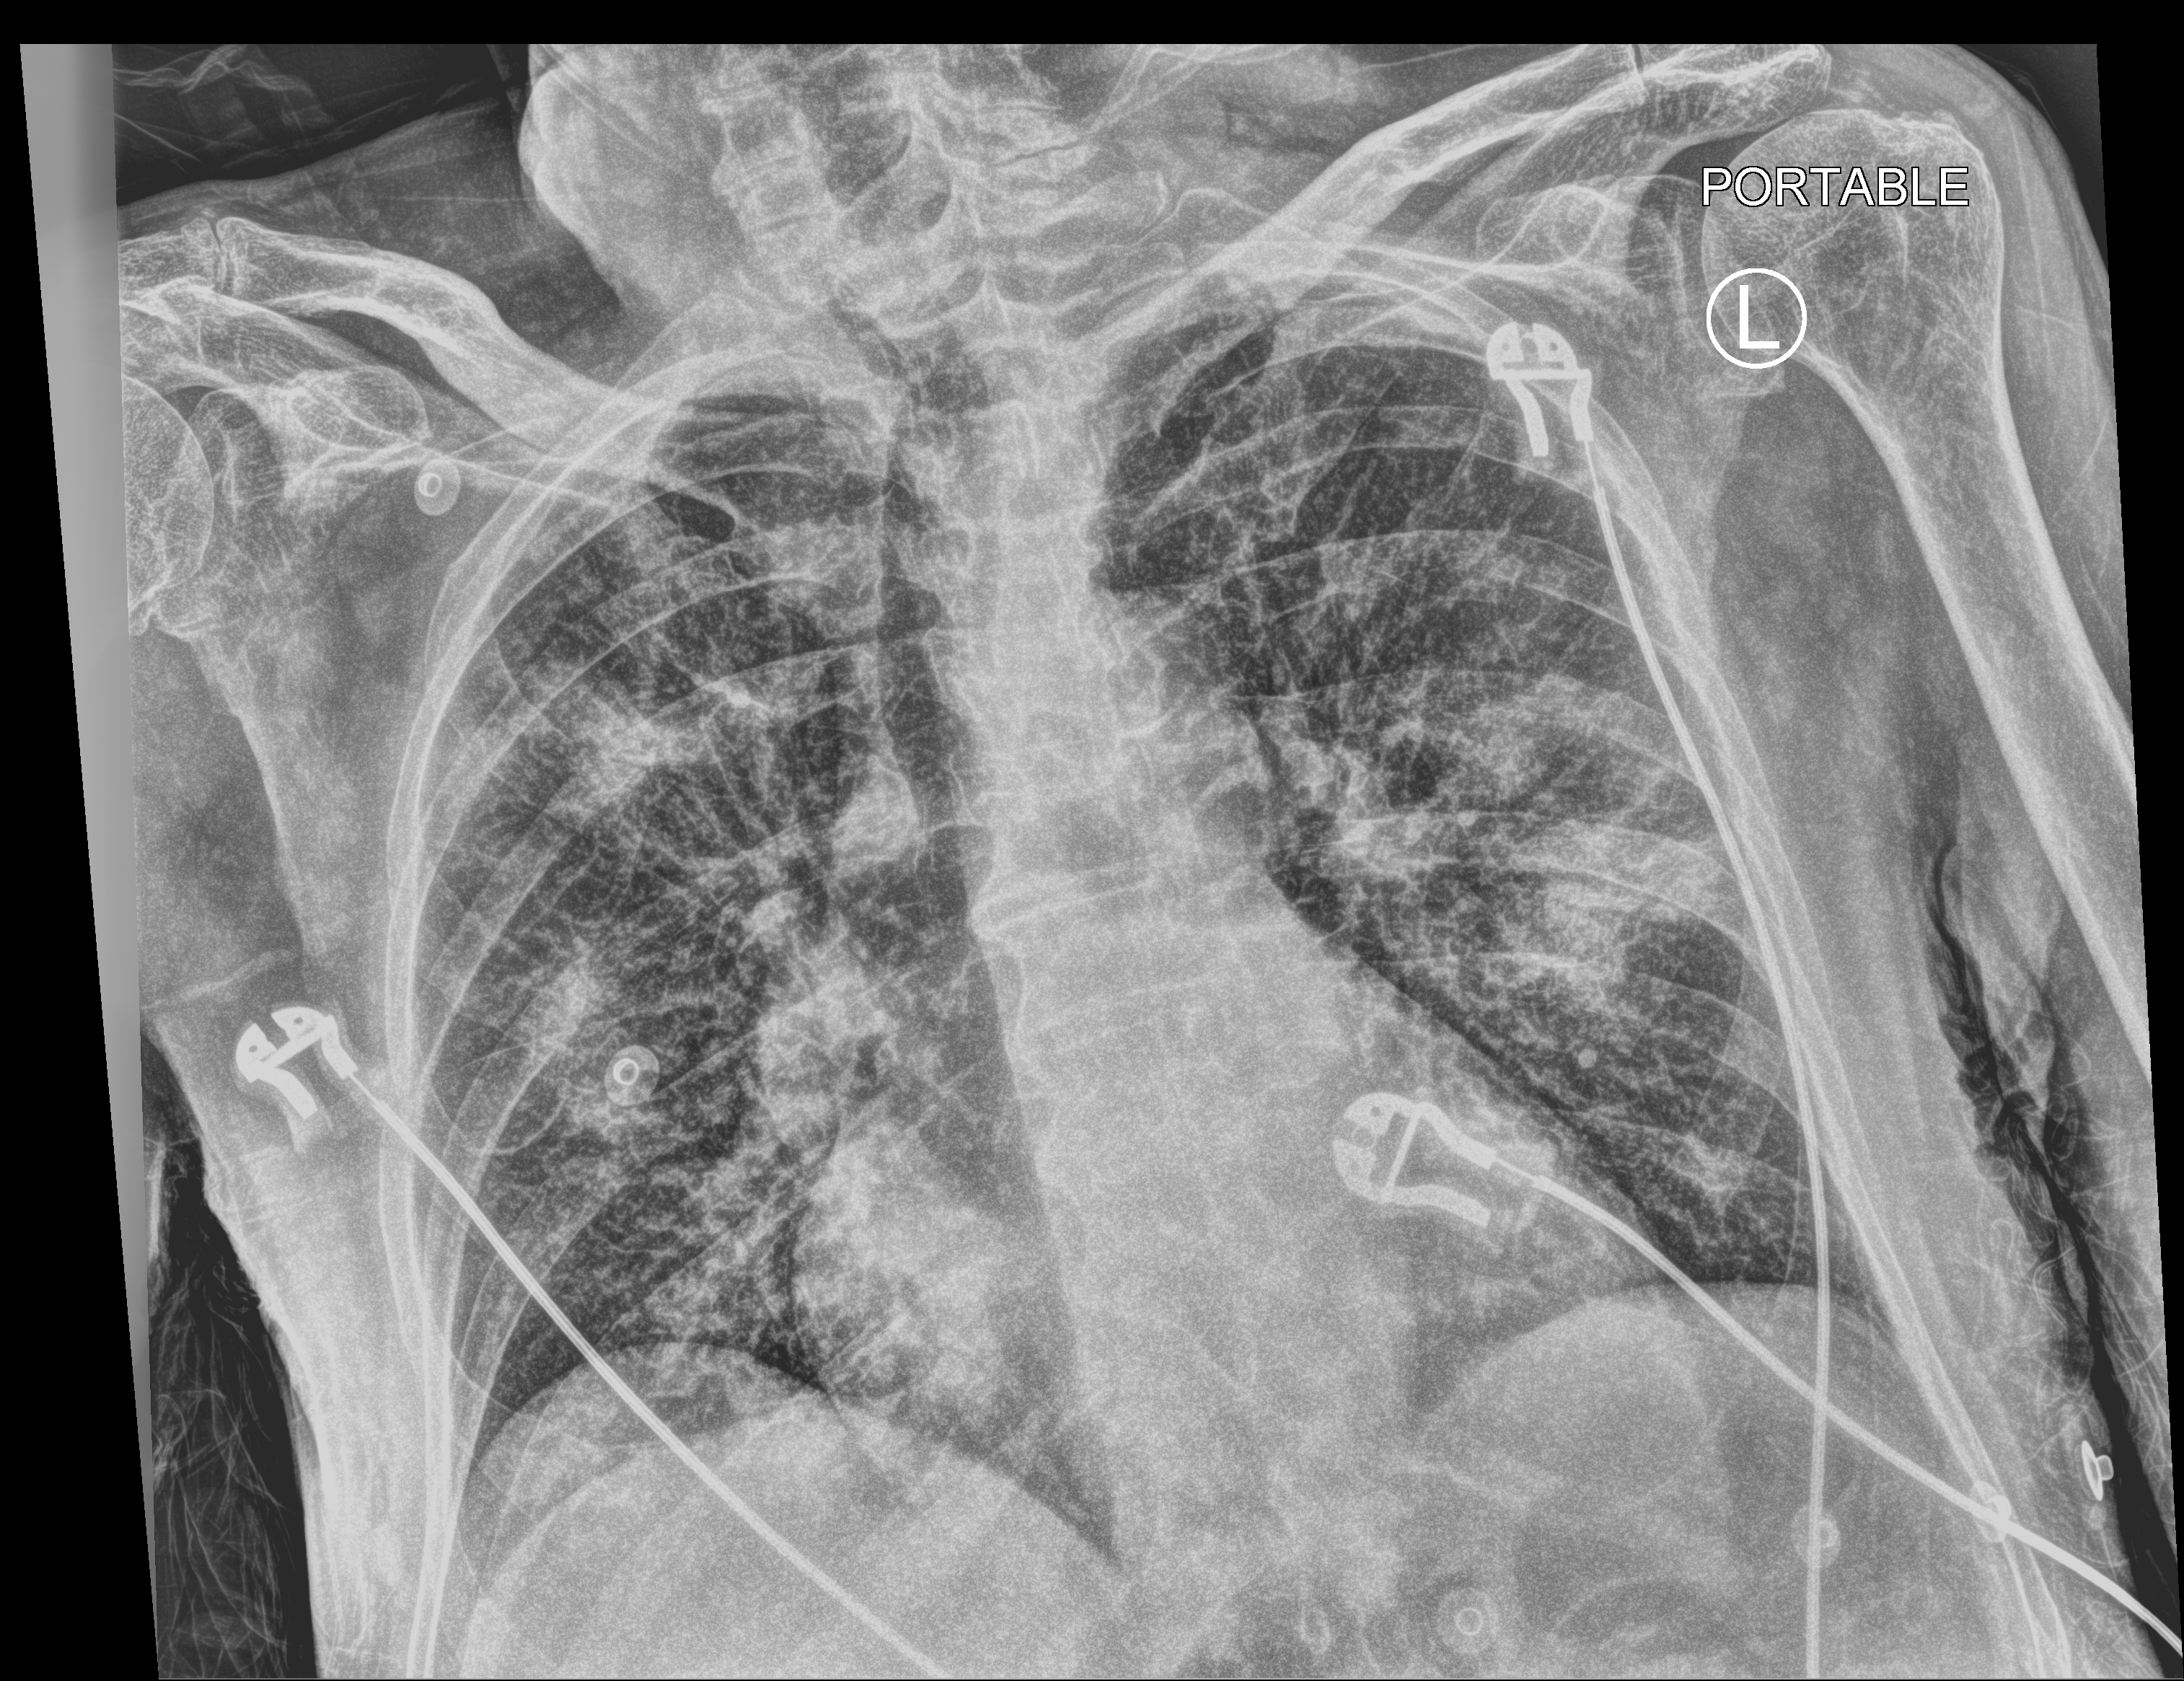
Chest X-ray (portable). Male patient hospitalised with COVID-19, age 75–90 years.
Admission-level facts for this patient (not findings on this image; timing relative to this image not recorded):
- hypertension (admission record): yes
- COPD (admission record): no